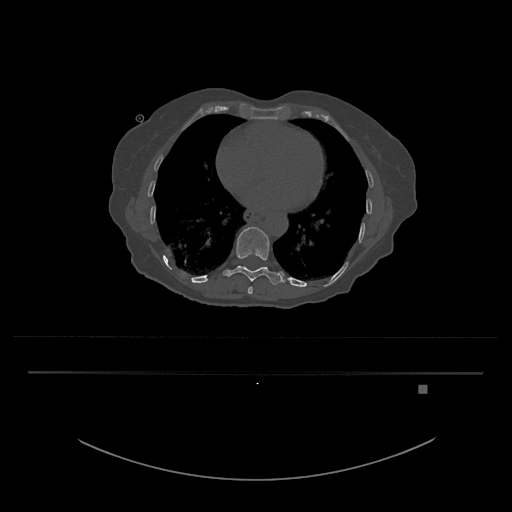
CT including the spine, one axial slice; position 714 of 797 along the scan axis; reconstruction kernel Br40s/3; bone window (W 1800 / L 400 HU); 0.5 mm slice thickness; 512 × 512 image matrix, field of view 500 × 500 mm. Female patient, age 57 years. From the clinical record (not read from this slice): primary cancer: cervical.
Outlined on this slice (semi-automatically segmented with operator editing):
- T10 vertebra: bounding box [x1, y1, x2, y2] px = [223, 227, 285, 285]
- T9 vertebra: [247, 287, 253, 294]